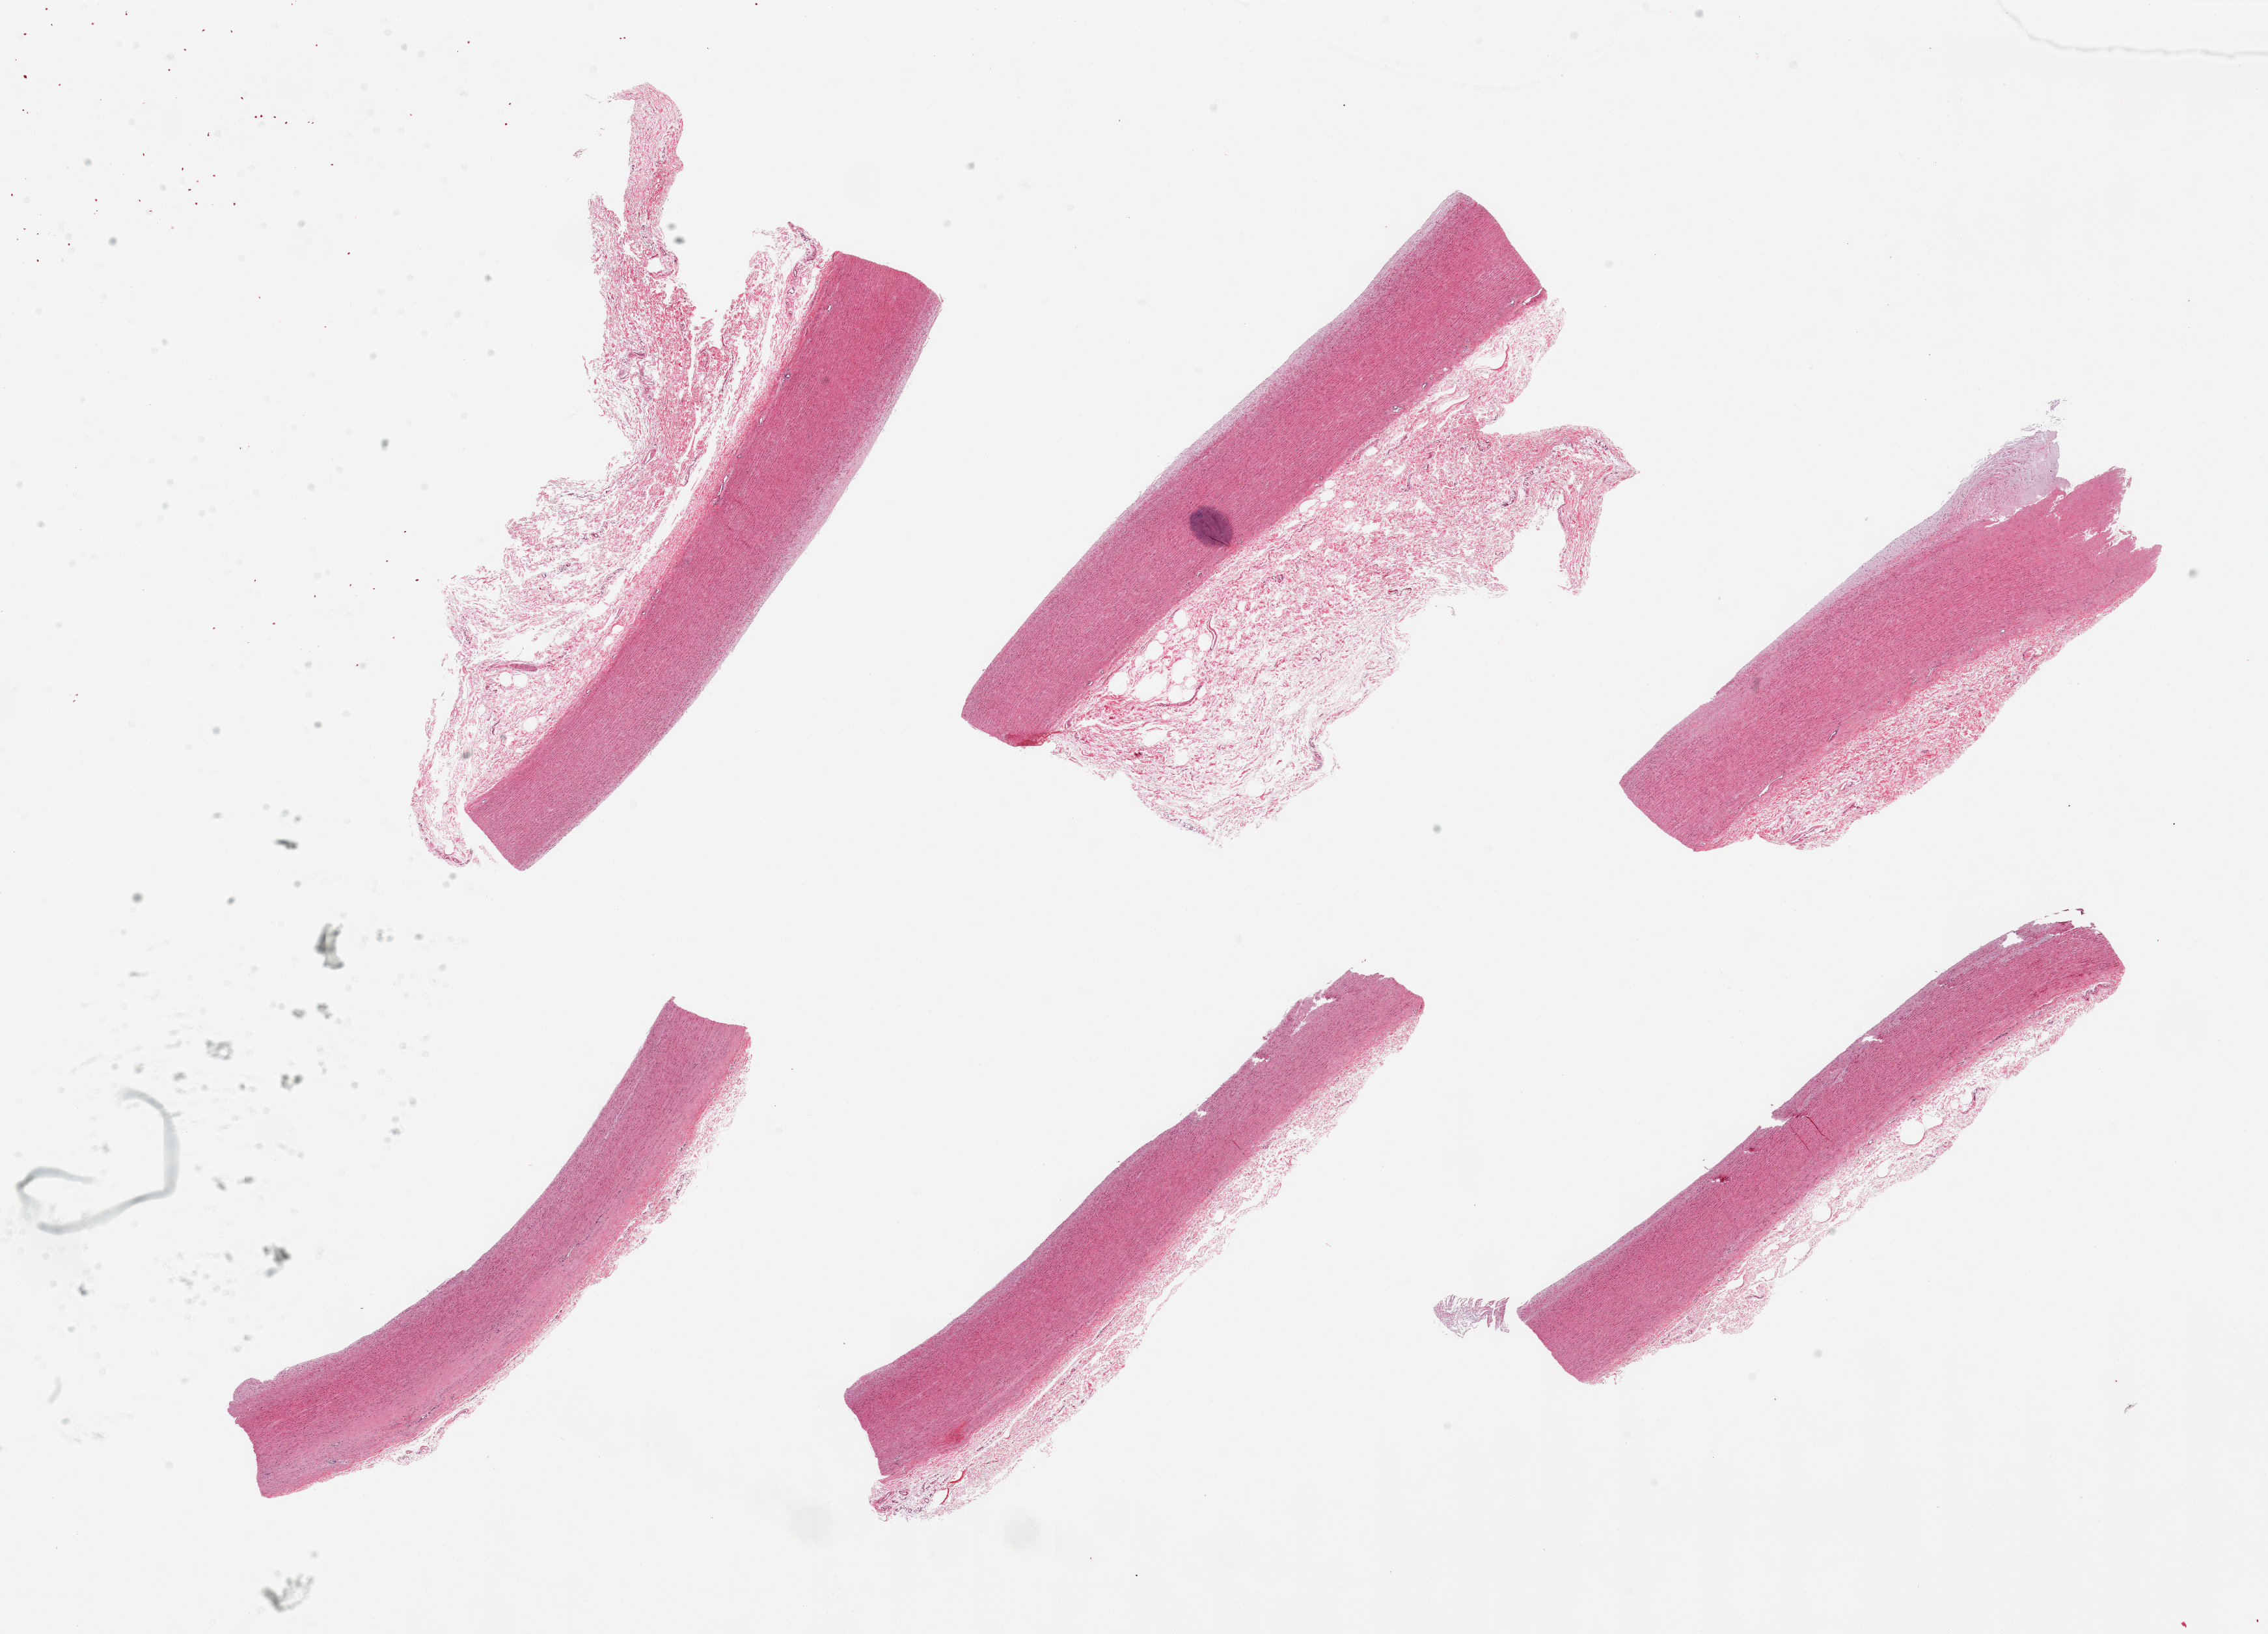
Whole-slide image, hematoxylin and eosin (H&E) stain, brightfield — low-resolution overview of the scanned area, about 27.6 x 19.9 mm; PAXgene-fixed, paraffin-embedded tissue; section of aorta (target tissue); tissue donor sample. Male donor.
- reviewer comment on this tissue sample: 6 pieces; AORTA not pancreas; up to 2mm periaortic stroma on 5 of 6 pieces